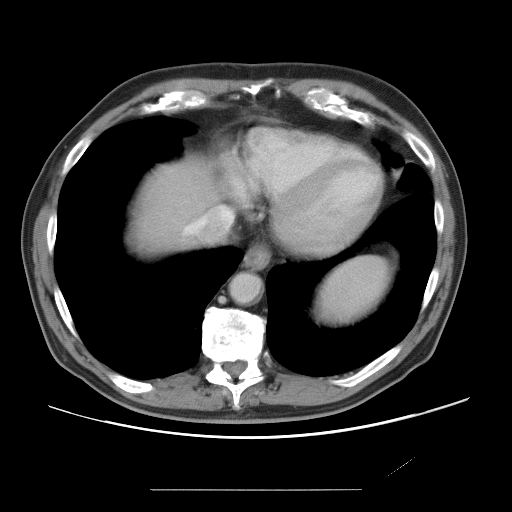
Contrast-enhanced abdominal CT, one axial slice; slice 68 of 87 in the series (ordered by position); 120 kVp; intravenous contrast given; soft-tissue window (W 400 / L 40 HU); 5 mm slice thickness; 512 × 512 image matrix, field of view 406 × 406 mm. Male patient, age 74 years. From the clinical record (not read from this slice): diagnosis: colorectal cancer liver metastases, imaged before liver resection; multiple liver metastases: yes; largest metastasis: 1.1 cm; disease in both lobes: no.
Structures marked on this image (manually delineated by an expert):
- liver: bounding box (x1, y1, x2, y2) in pixels: (131, 161, 216, 254)
- planned liver remnant (the part of the liver to remain after resection): (131, 160, 217, 254)